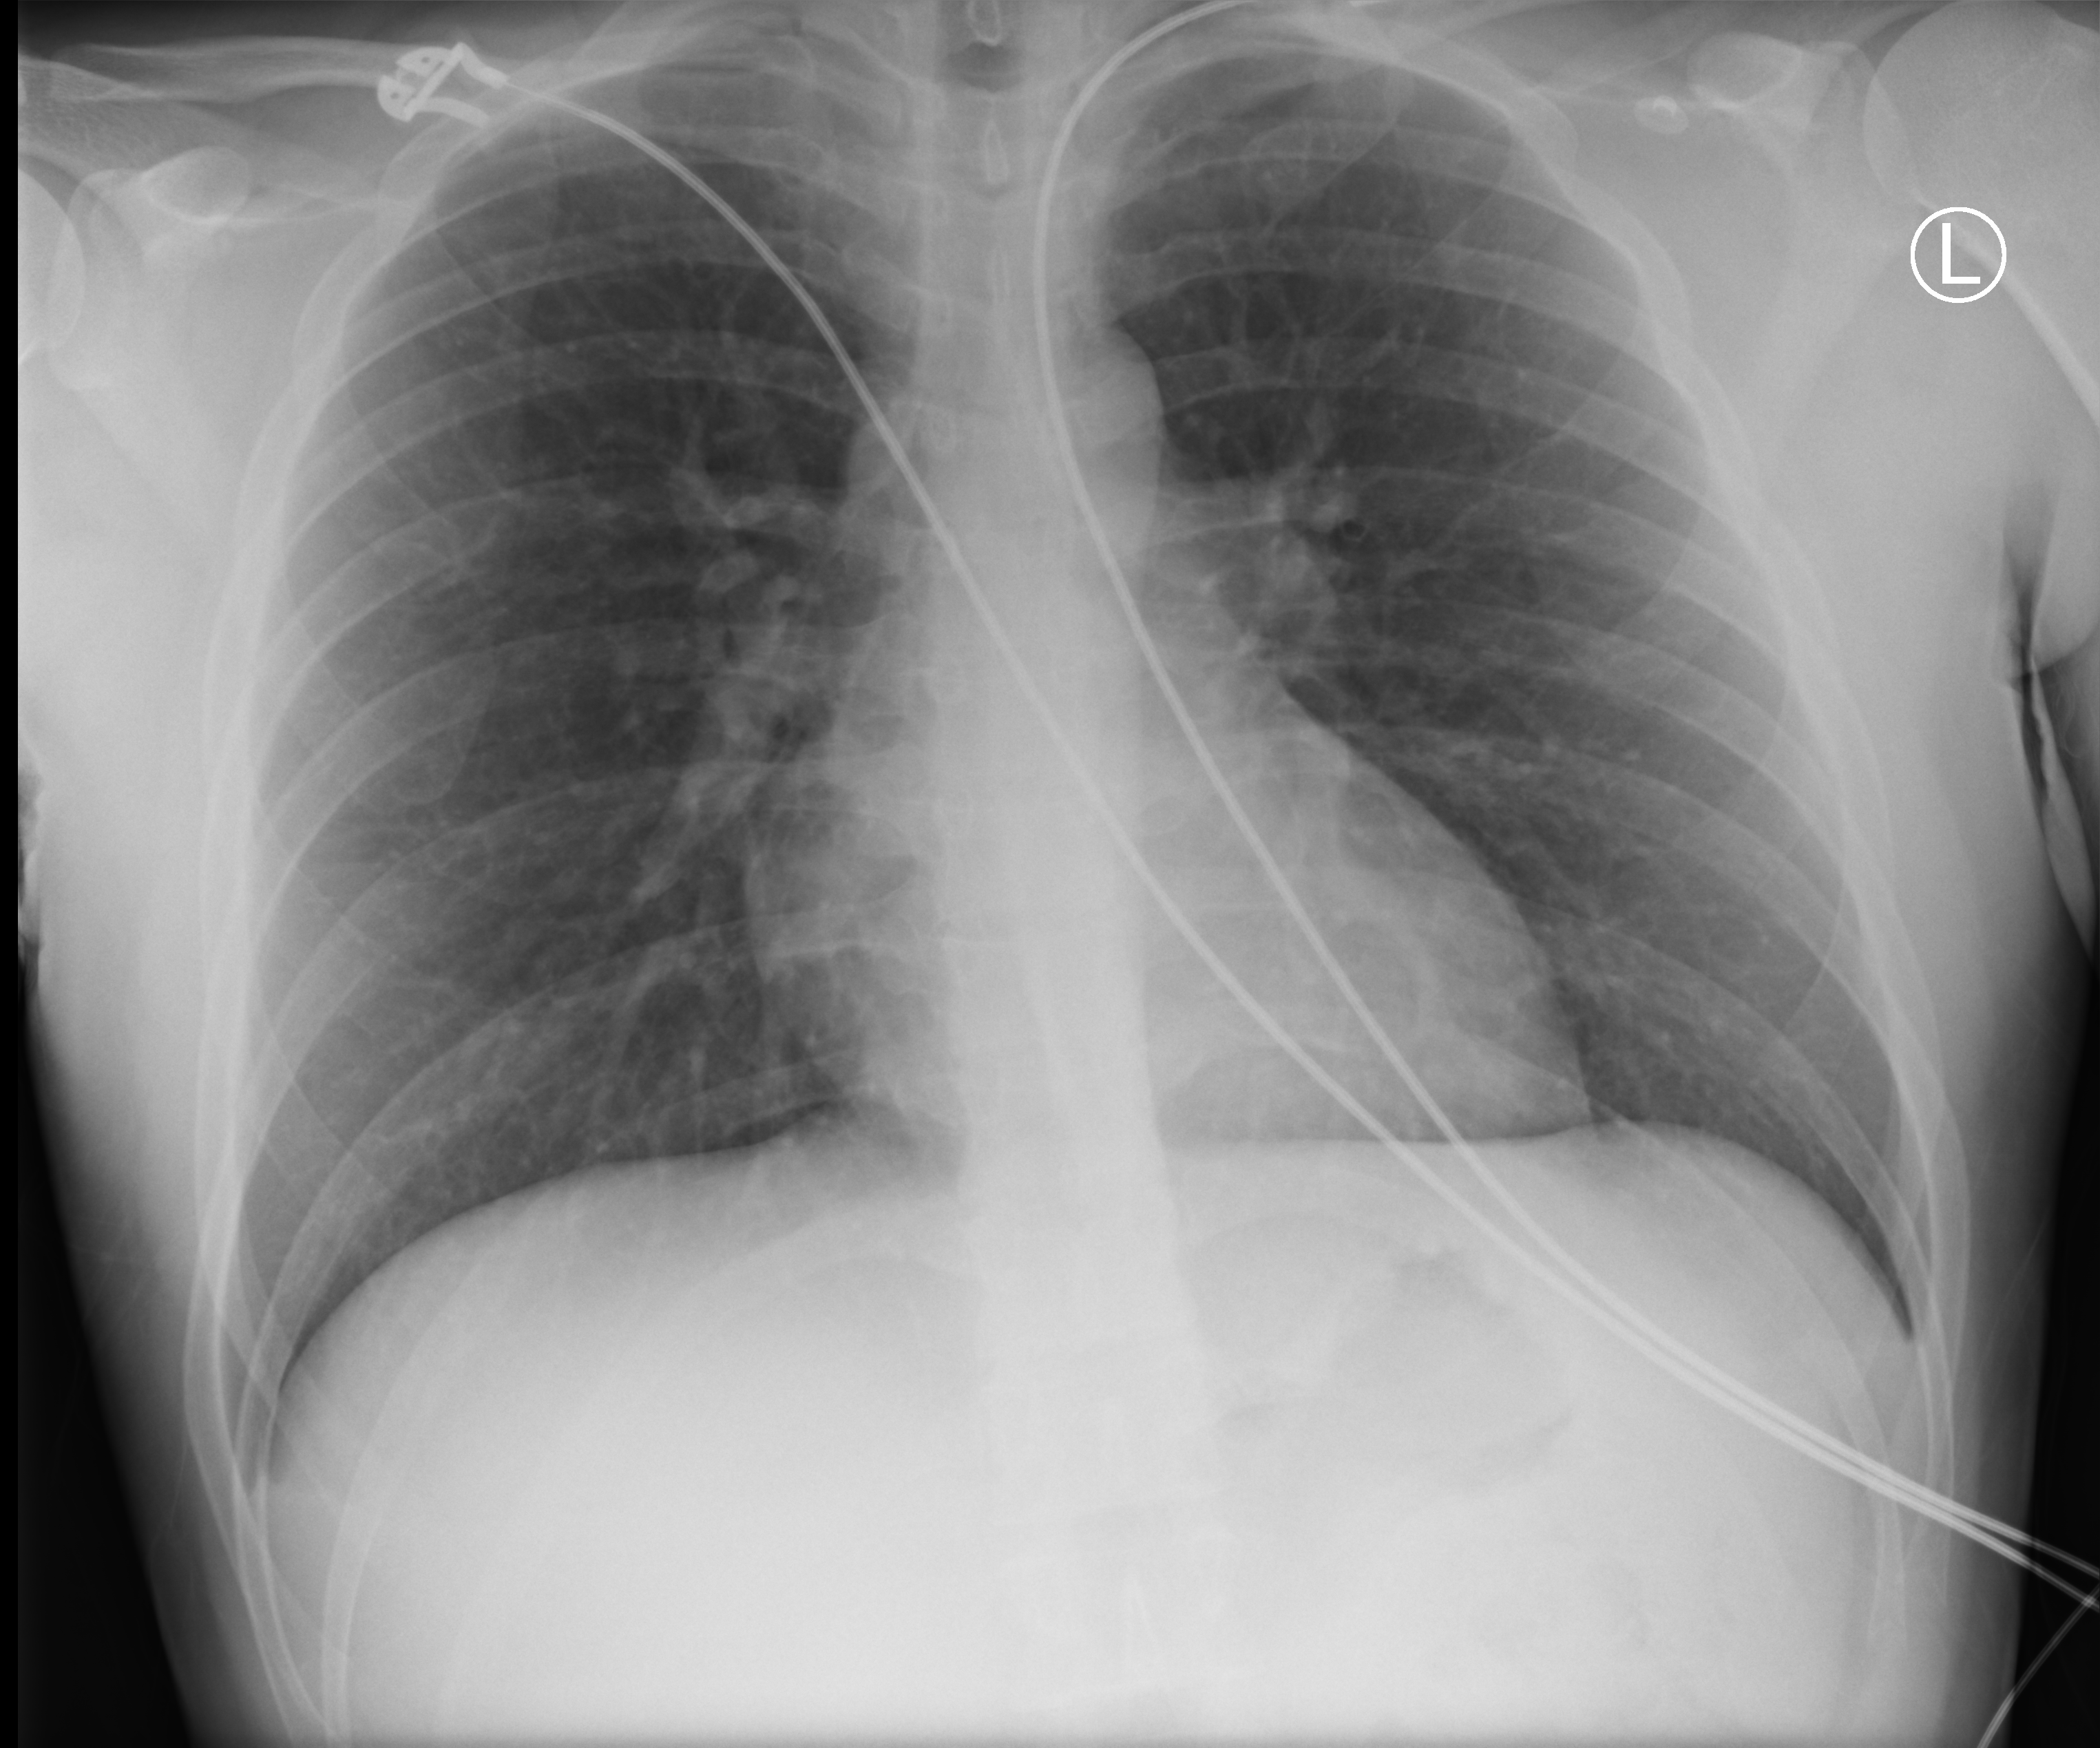
Portable chest radiograph; anteroposterior (AP) projection. Patient hospitalised with COVID-19; male, aged 18–59 years.
Admission-level facts for this patient (not findings on this image; timing relative to this image not recorded): admitted to intensive care during this hospital stay: no; length of hospital stay: 1 day; mechanically ventilated during this hospital stay: no.